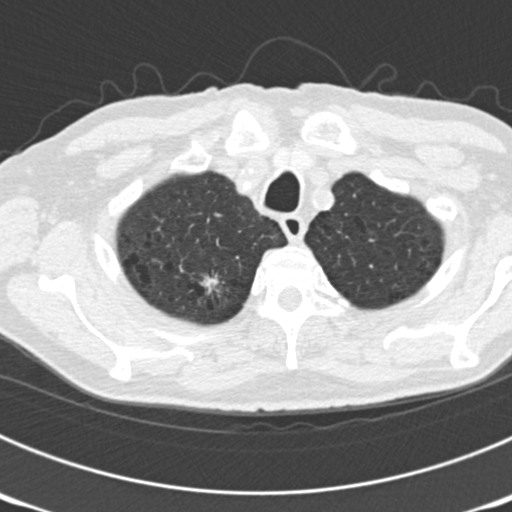
Low-dose screening chest CT, one axial slice. Position 157 of 177 along the scan axis. 120 kVp. Lung window (W 1500 / L -600 HU). 512 × 512 image matrix, field of view 300 × 300 mm.
Structures marked on this image (expert manual segmentation):
- lesion 3 (nodule, upper lobe of right lung): bounding box <200,275,221,292> (left, top, right, bottom; pixels)